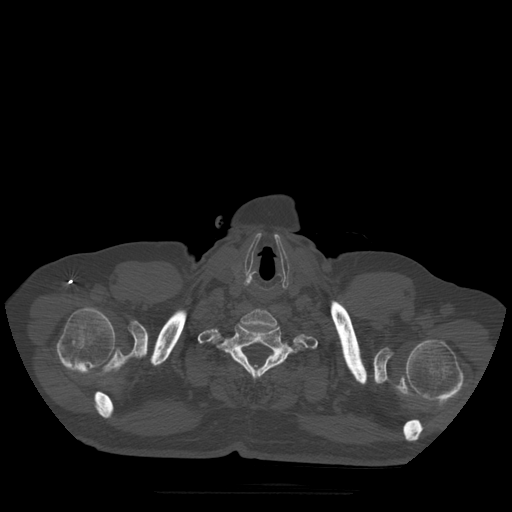
CT including the spine, one axial slice. Position 440 of 522 along the scan axis. Bone window (W 1800 / L 400 HU). 1.25 mm slice thickness. 512 × 512 image matrix, field of view 420 × 420 mm. Patient age 72 years. Case-level facts recorded for this patient, not image findings: primary cancer: prostate.
Annotated regions visible in this slice (semi-automatic segmentation, software-assisted and operator-edited):
- T1 vertebra: bounding box <211,324,304,377> (left, top, right, bottom; pixels)
- T2 vertebra: <297,367,303,372>